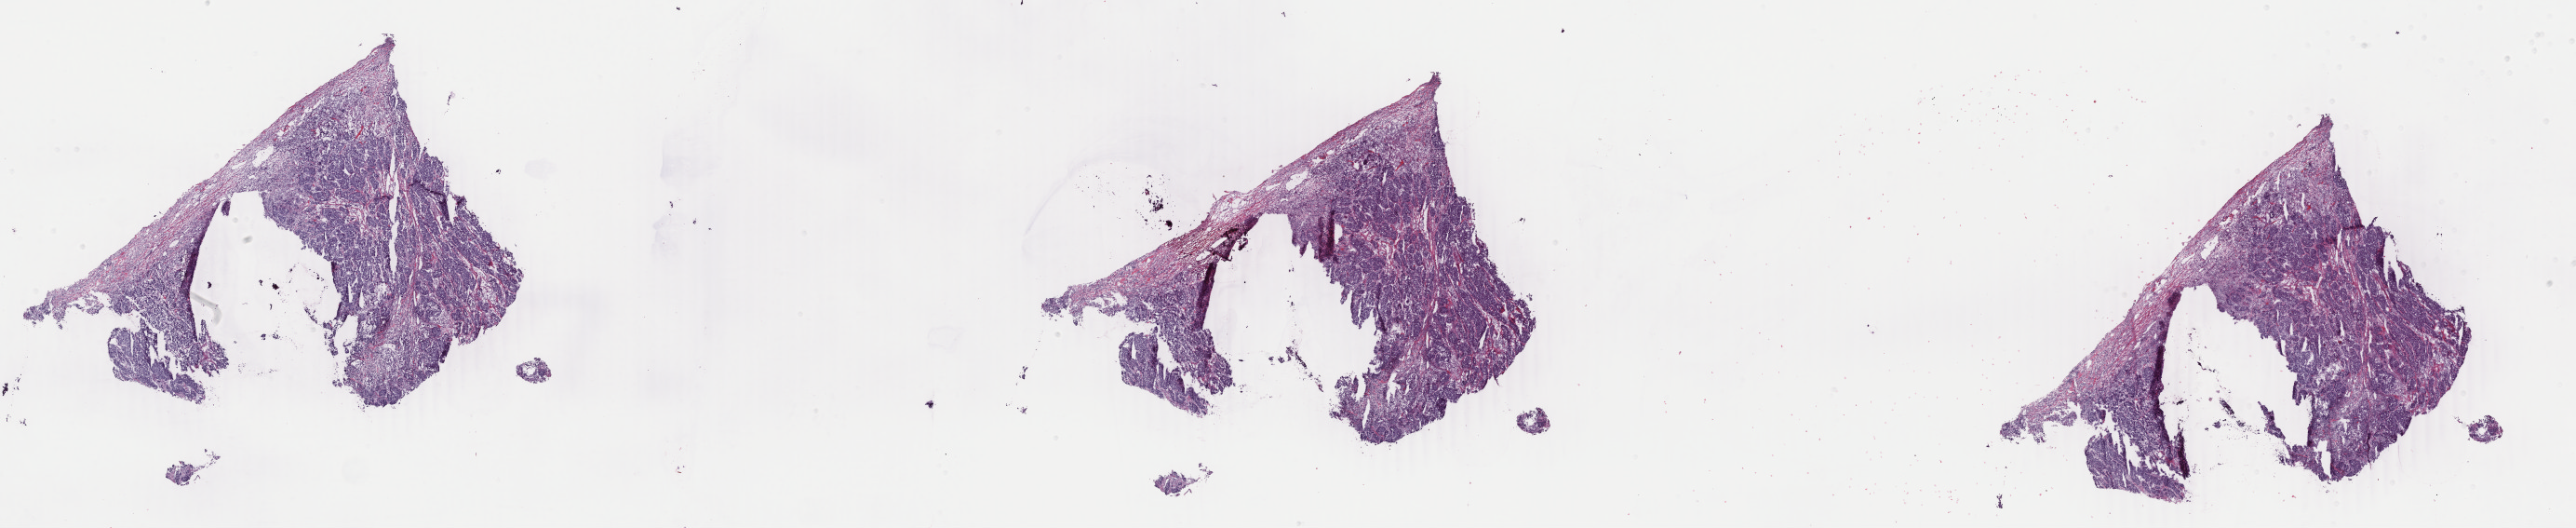
H&E whole-slide image, a low-resolution overview of the entire scanned area, about 44.0 x 9.0 mm, frozen section, breast, primary tumour sample. Female, age 56 years at initial diagnosis. Slide review estimates, as recorded: tumour cells 85%, tumour nuclei 85%.
Diagnosis: Infiltrating duct carcinoma, NOS.